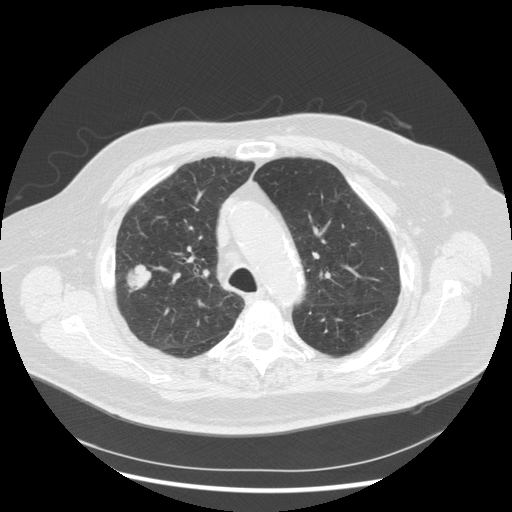
Low-dose screening chest CT, one axial slice. Slice 204 of 263 in the series (ordered by position). Lung window (W 1500 / L -600 HU). 2.5 mm slice thickness. 512 × 512 image matrix.
Structures marked on this image (expert manual segmentation):
- lesion 1 (tumor, upper lobe of right lung): bounding box <128,265,151,291> (left, top, right, bottom; pixels)